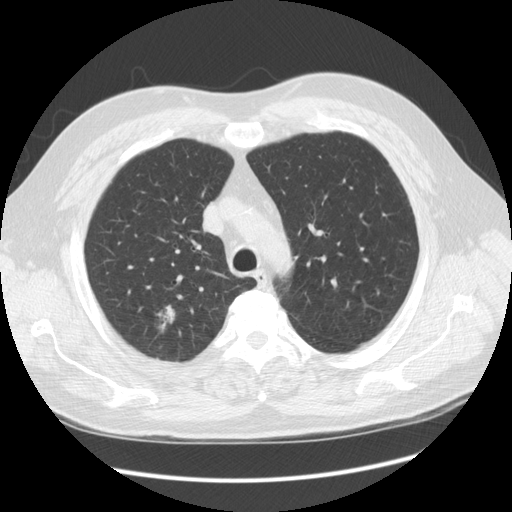
Low-dose screening chest CT, one axial slice; slice 83 of 108 in the series (ordered by position); 120 kVp; lung window (W 1500 / L -600 HU); 512 × 512 image matrix, field of view 380 × 380 mm.
Annotated regions visible in this slice (outlined manually by an expert reader):
- lesion 1 (tumor, upper lobe of right lung): box from (x=157, y=305) to (x=175, y=332) px